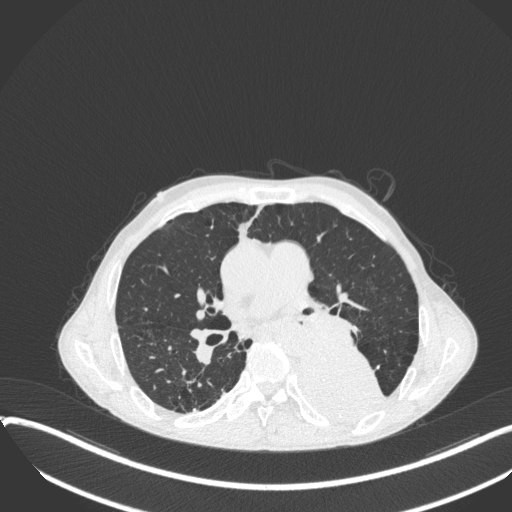
Chest CT, one axial slice; slice 205 of 400 in the series (ordered by position); reconstruction kernel B31f; lung window (W 1500 / L -600 HU); 1 mm slice thickness; 512 × 512 image matrix, field of view 400 × 400 mm. Male patient, age 57 years. Case-level facts recorded for this patient, not image findings: clinical TNM (as recorded): T4 N0 M0.
Outlined on this slice (rectangle marked by the reading radiologist):
- lung tumour (recorded histology: squamous cell carcinoma): bounding box [x1, y1, x2, y2] px = [300, 336, 386, 425]